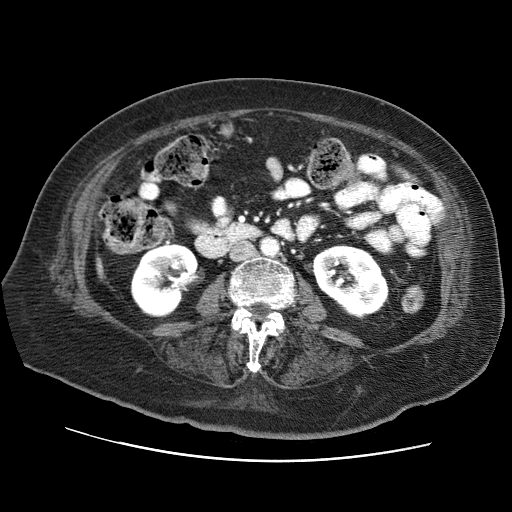
Contrast-enhanced abdominal CT (liver protocol), one axial slice; slice 12 of 73 in the series (ordered by position); 120 kVp; soft-tissue window (W 400 / L 40 HU); 2.5 mm slice thickness; 512 × 512 image matrix. Case-level facts recorded for this patient, not image findings: diagnosis: hepatocellular carcinoma (patient treated with transarterial chemoembolisation; whether this scan precedes or follows treatment is not stated here); TNM stage (as recorded): Stage-I; Child-Pugh class: A; tumour differentiation: well differentiated; tumour nodularity: uninodular.
Structures marked on this image (semi-automatically segmented with operator editing):
- liver parenchyma outside the tumour (the mass and vessels are separate outlines, so this box may not span the whole liver): box from (x=96, y=257) to (x=104, y=277) px